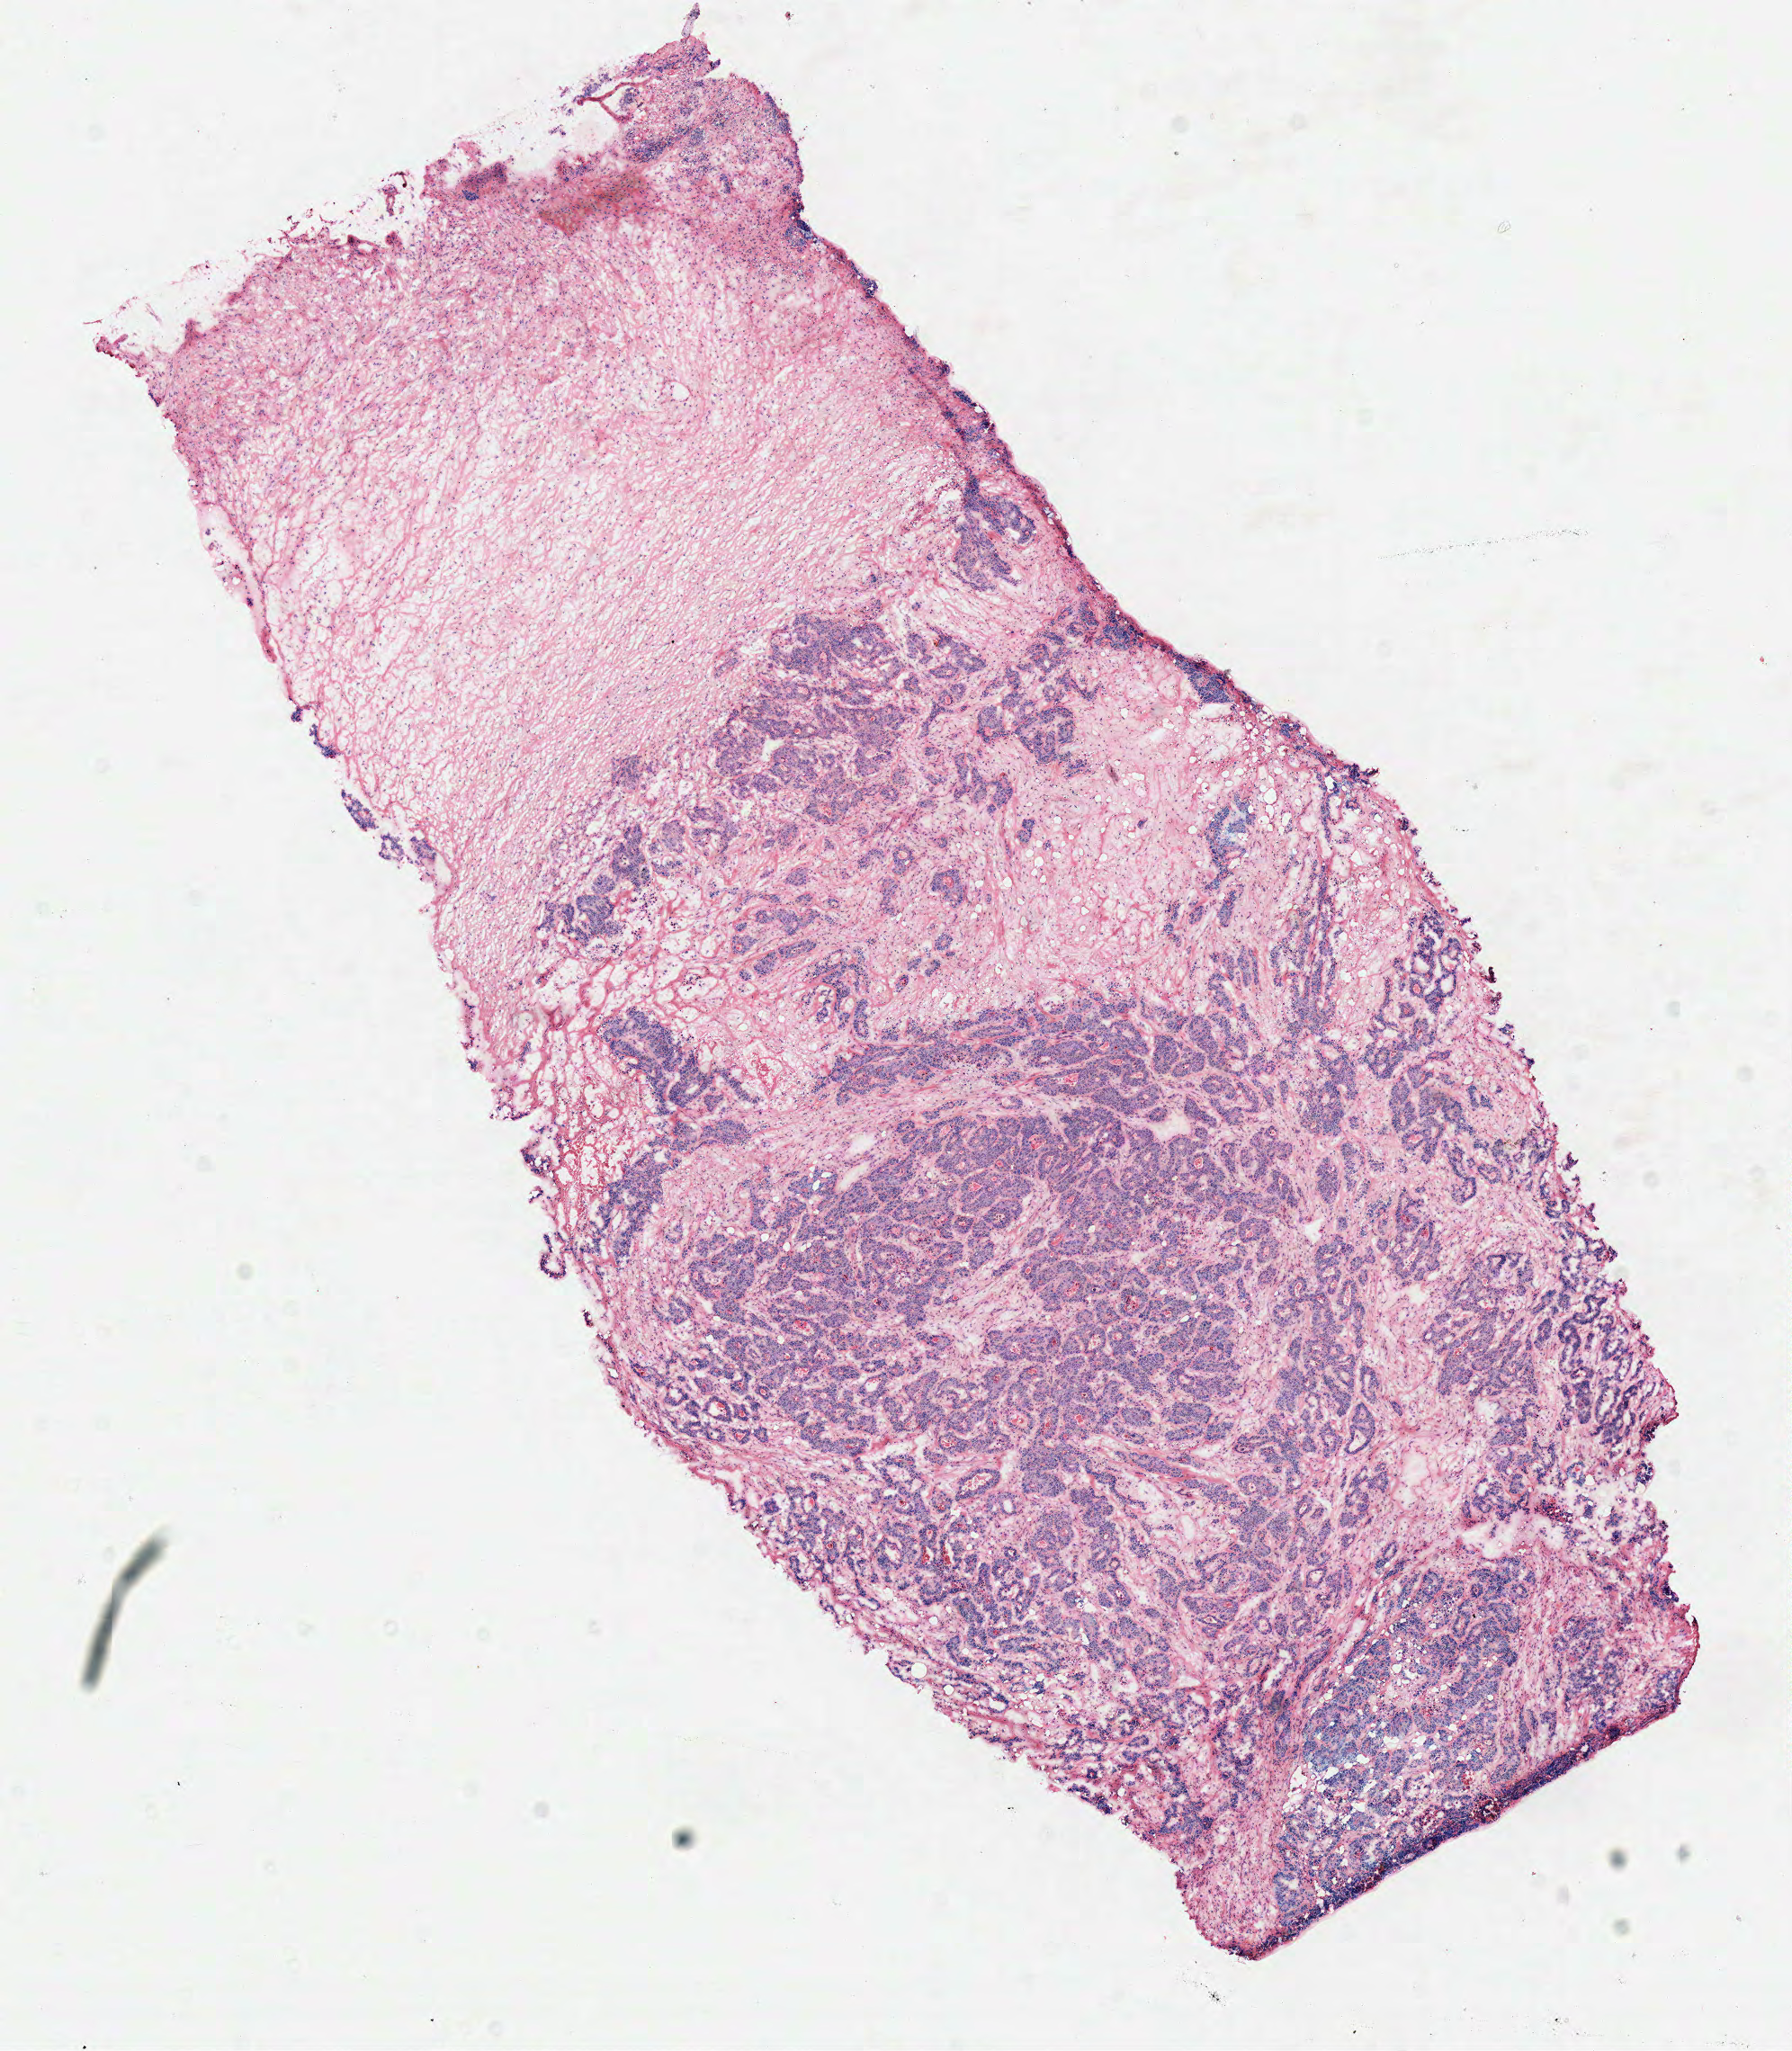
Digitized Hematoxylin and eosin (H&E) stained tissue section (whole slide) — low-resolution overview of the scanned area, about 7.8 x 9.0 mm (slide scanned at 40x); frozen section; sample: primary tumour, rectum. Male patient; age at initial diagnosis 53 years. Slide review estimates, as recorded: tumour cells 55%, tumour nuclei 80%.
Pathologic diagnosis: Adenocarcinoma in tubulovillous adenoma.